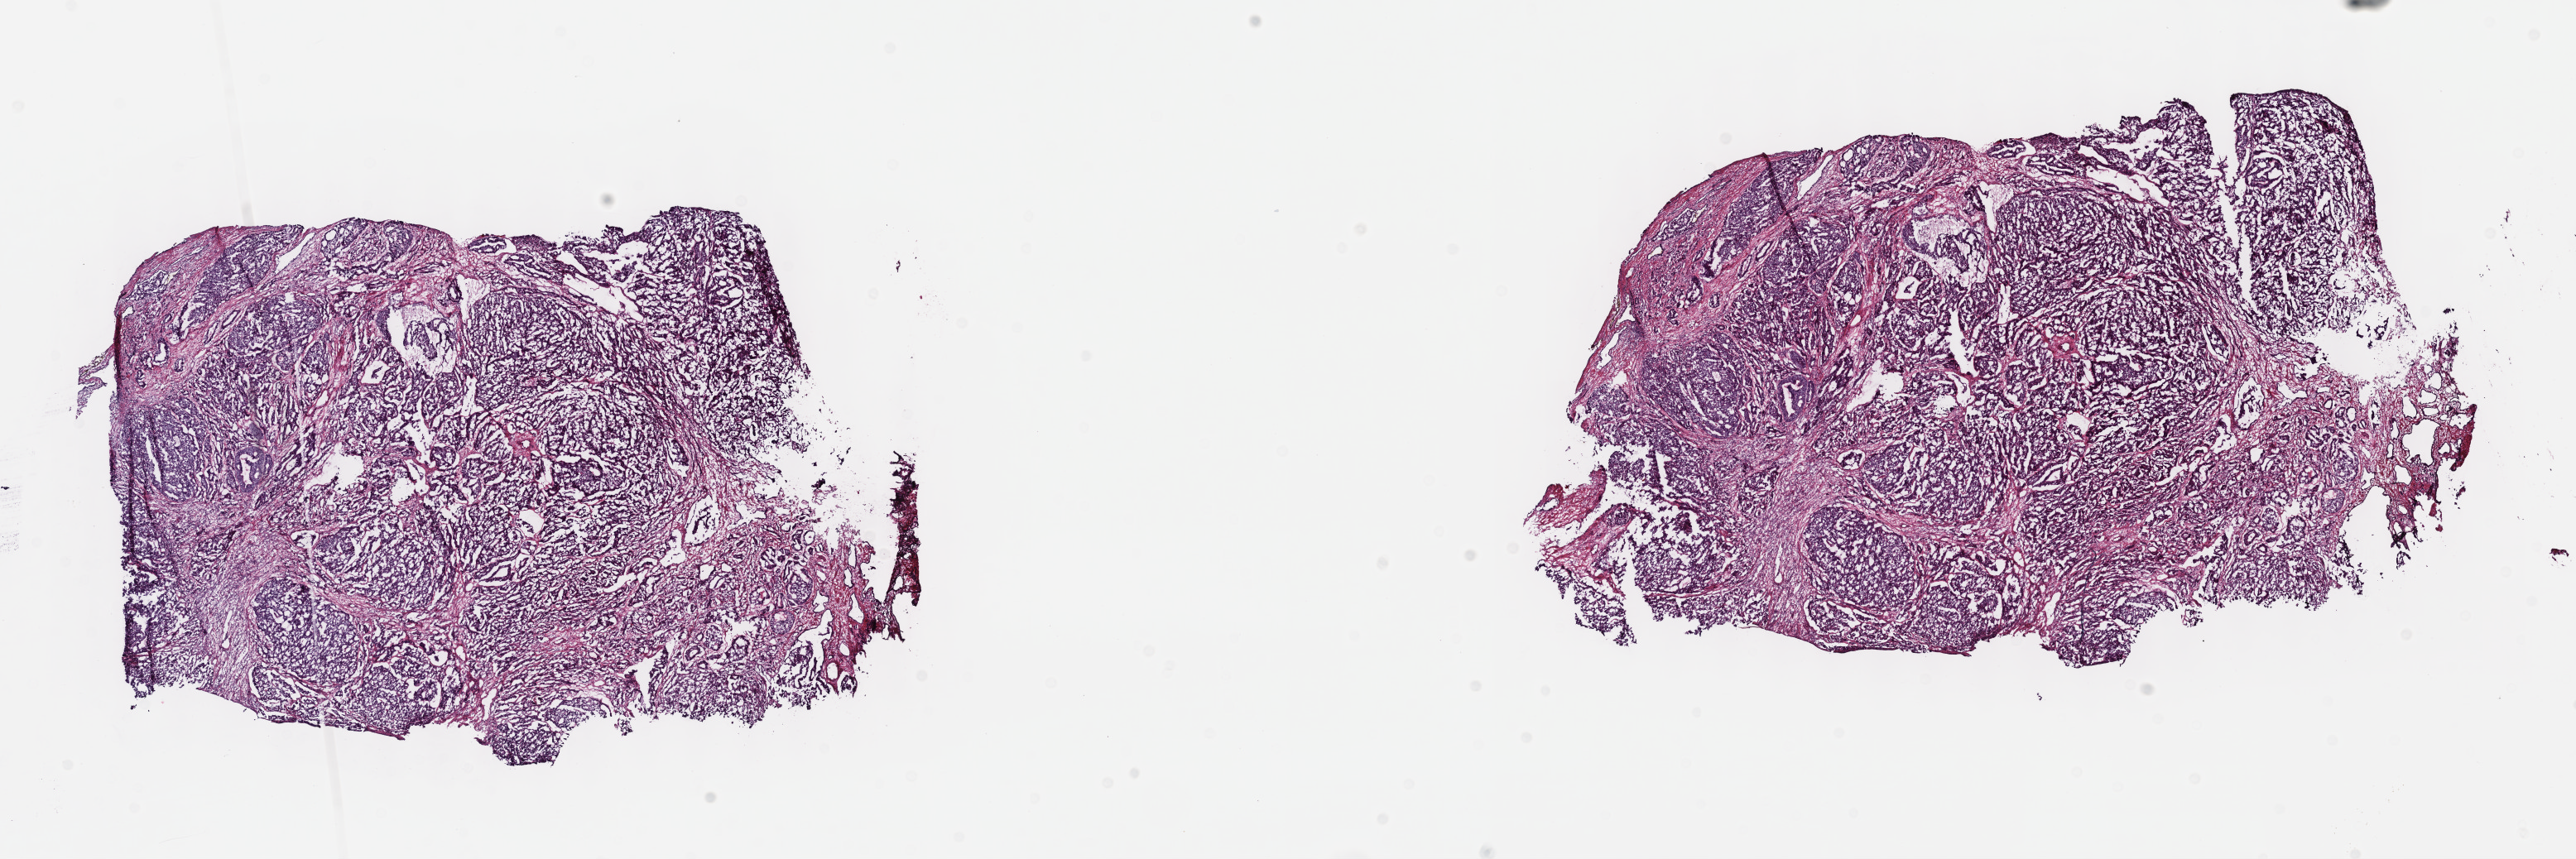
Whole-slide histology image, H&E — whole scanned area (about 25.2 x 8.4 mm, acquisition: 40x scan) shown as a low-resolution overview, frozen section, primary tumour sample from the prostate. Patient: male, age at initial diagnosis 56 years. Gleason score: 9 (4+5). Pathologist review of this section (percent, as recorded): tumour cells 62%, tumour nuclei 85%, normal cells 0%, stromal cells 35%, necrosis 3%. Inflammatory infiltration, as recorded: lymphocyte infiltration 7%, monocyte infiltration 3%, neutrophil infiltration 1%.
Diagnosis: Adenocarcinoma, NOS (prostate gland).